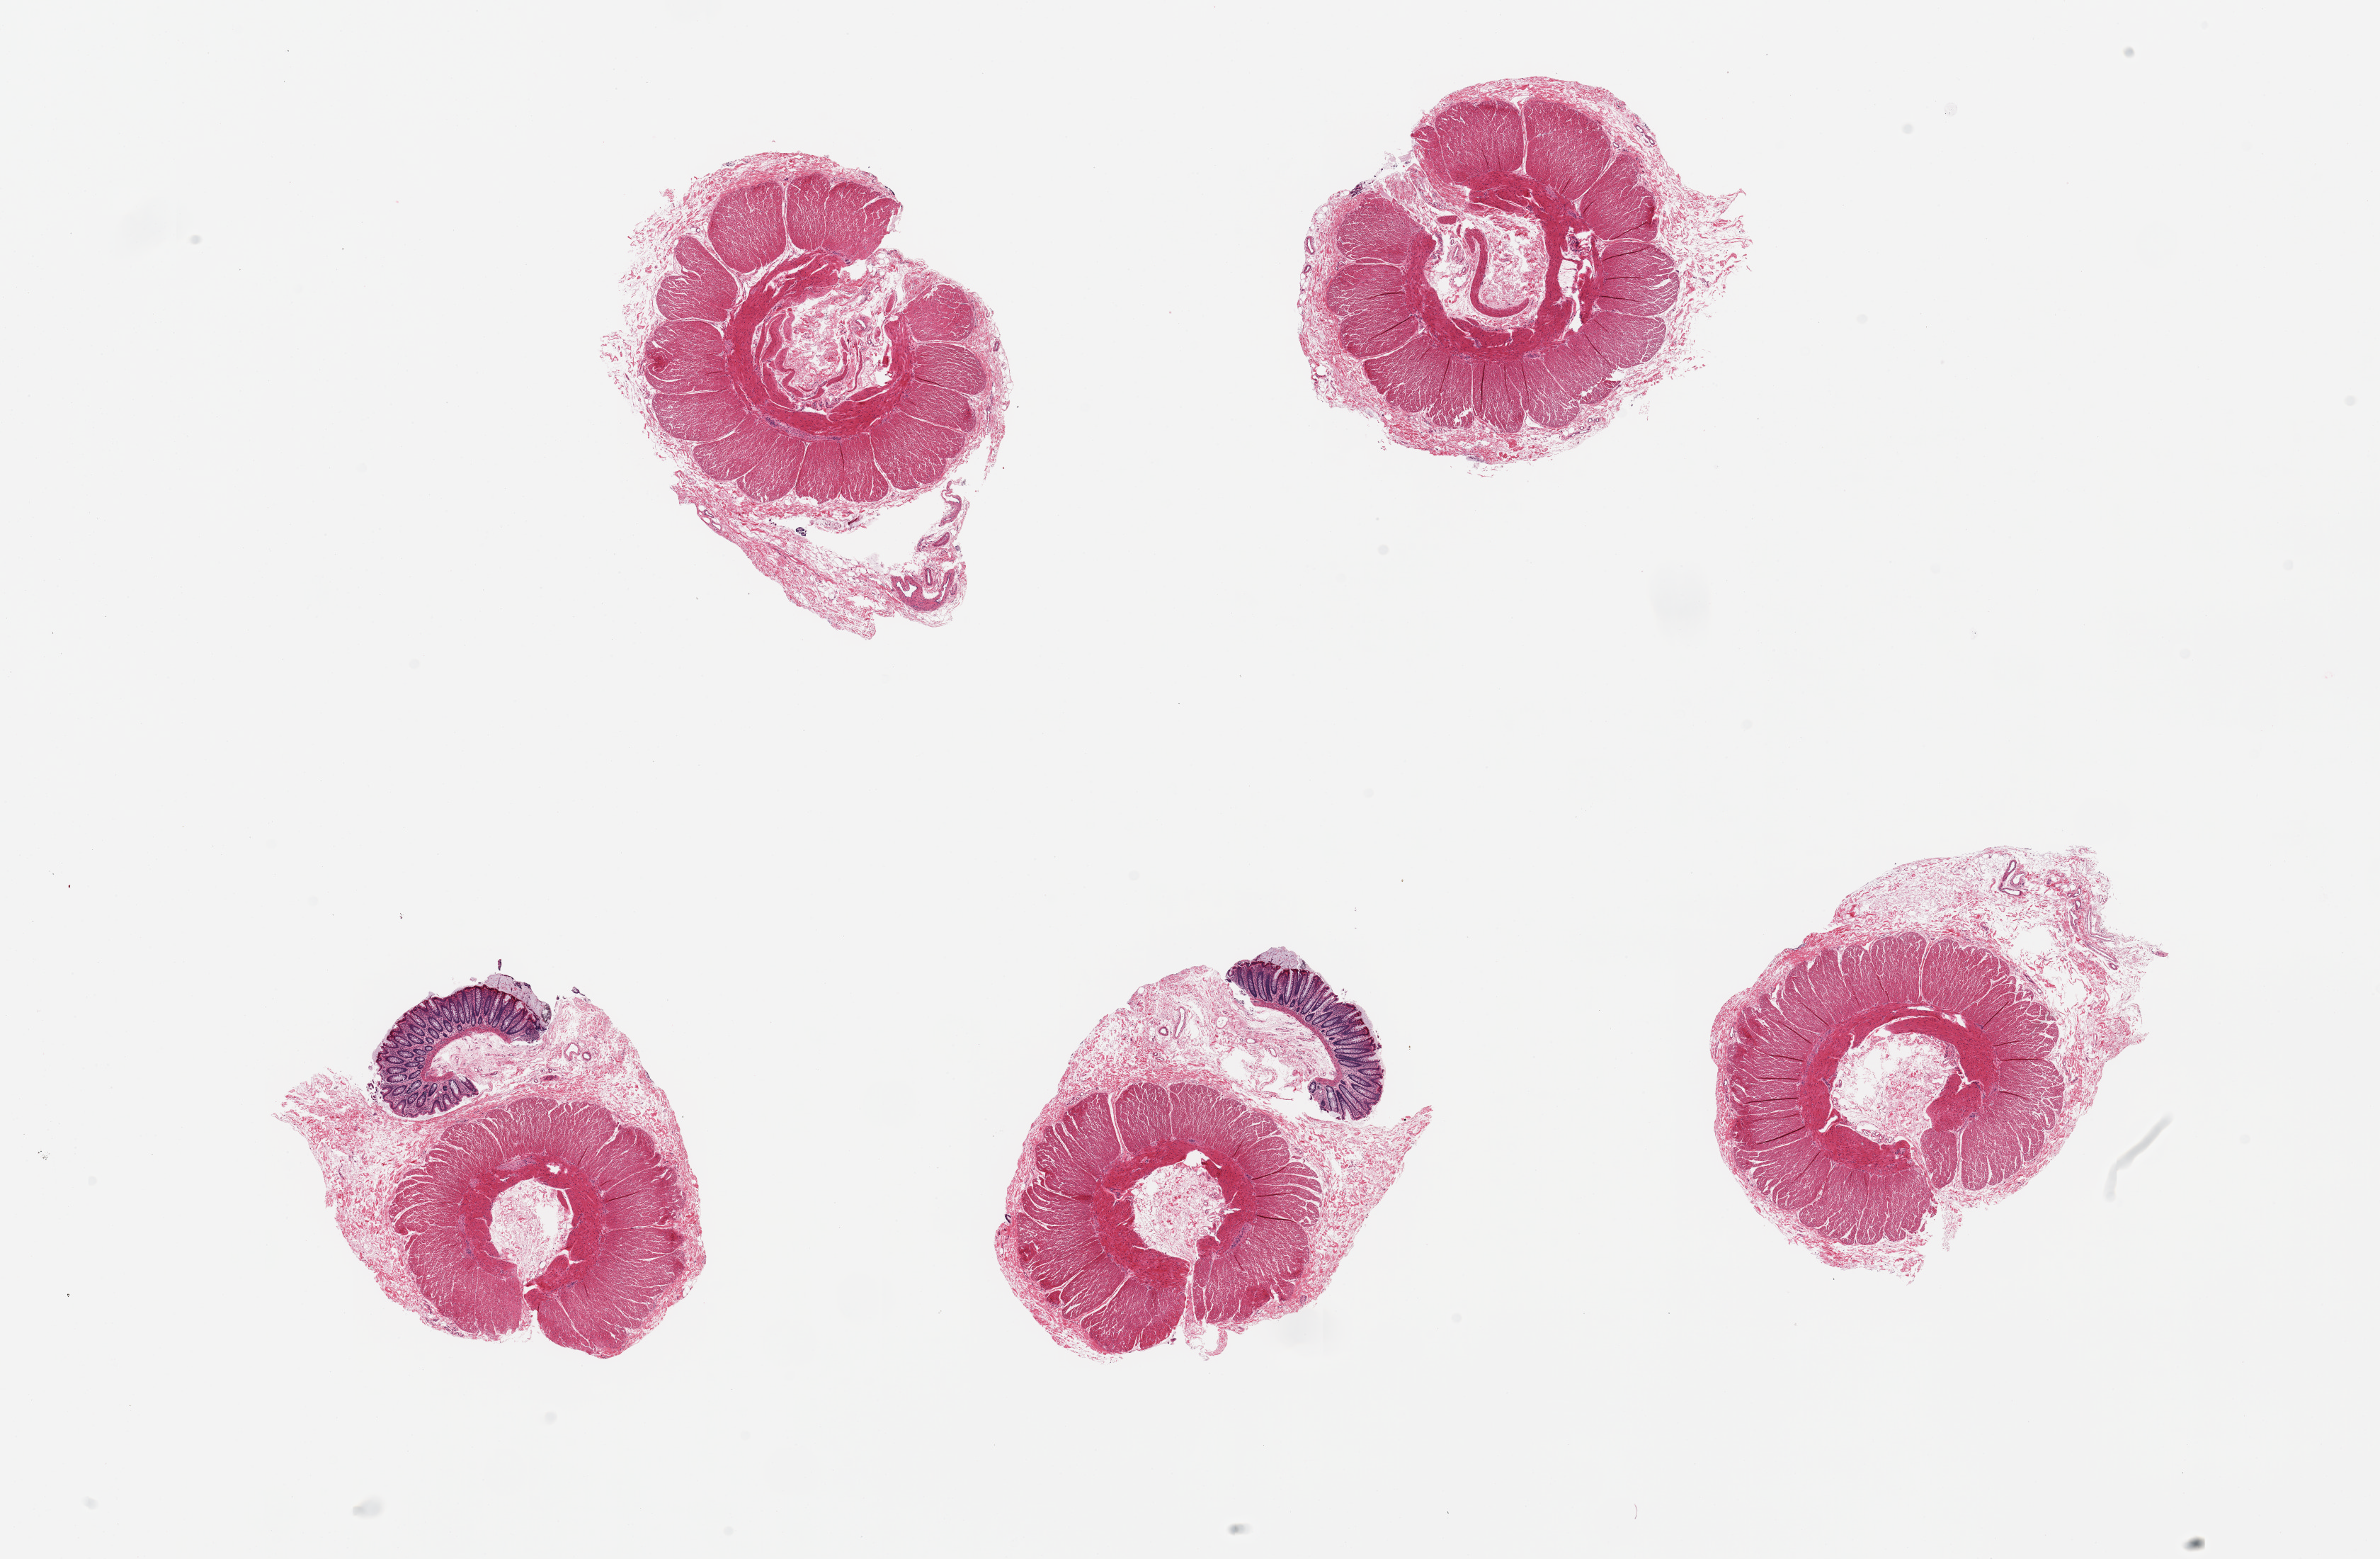
Whole-slide image, H&E stain — shown as a low-resolution overview of the whole scanned area (about 26.6 x 17.4 mm, slide scanned at 20x); PAXgene-fixed, paraffin-embedded tissue; sampled site (target tissue): sigmoid colon; donor tissue sample. Donor sex: female.
Reviewer comment on this tissue sample: 5 pieces; muscularis and submucosa, 2 with residual strips of mucosa.